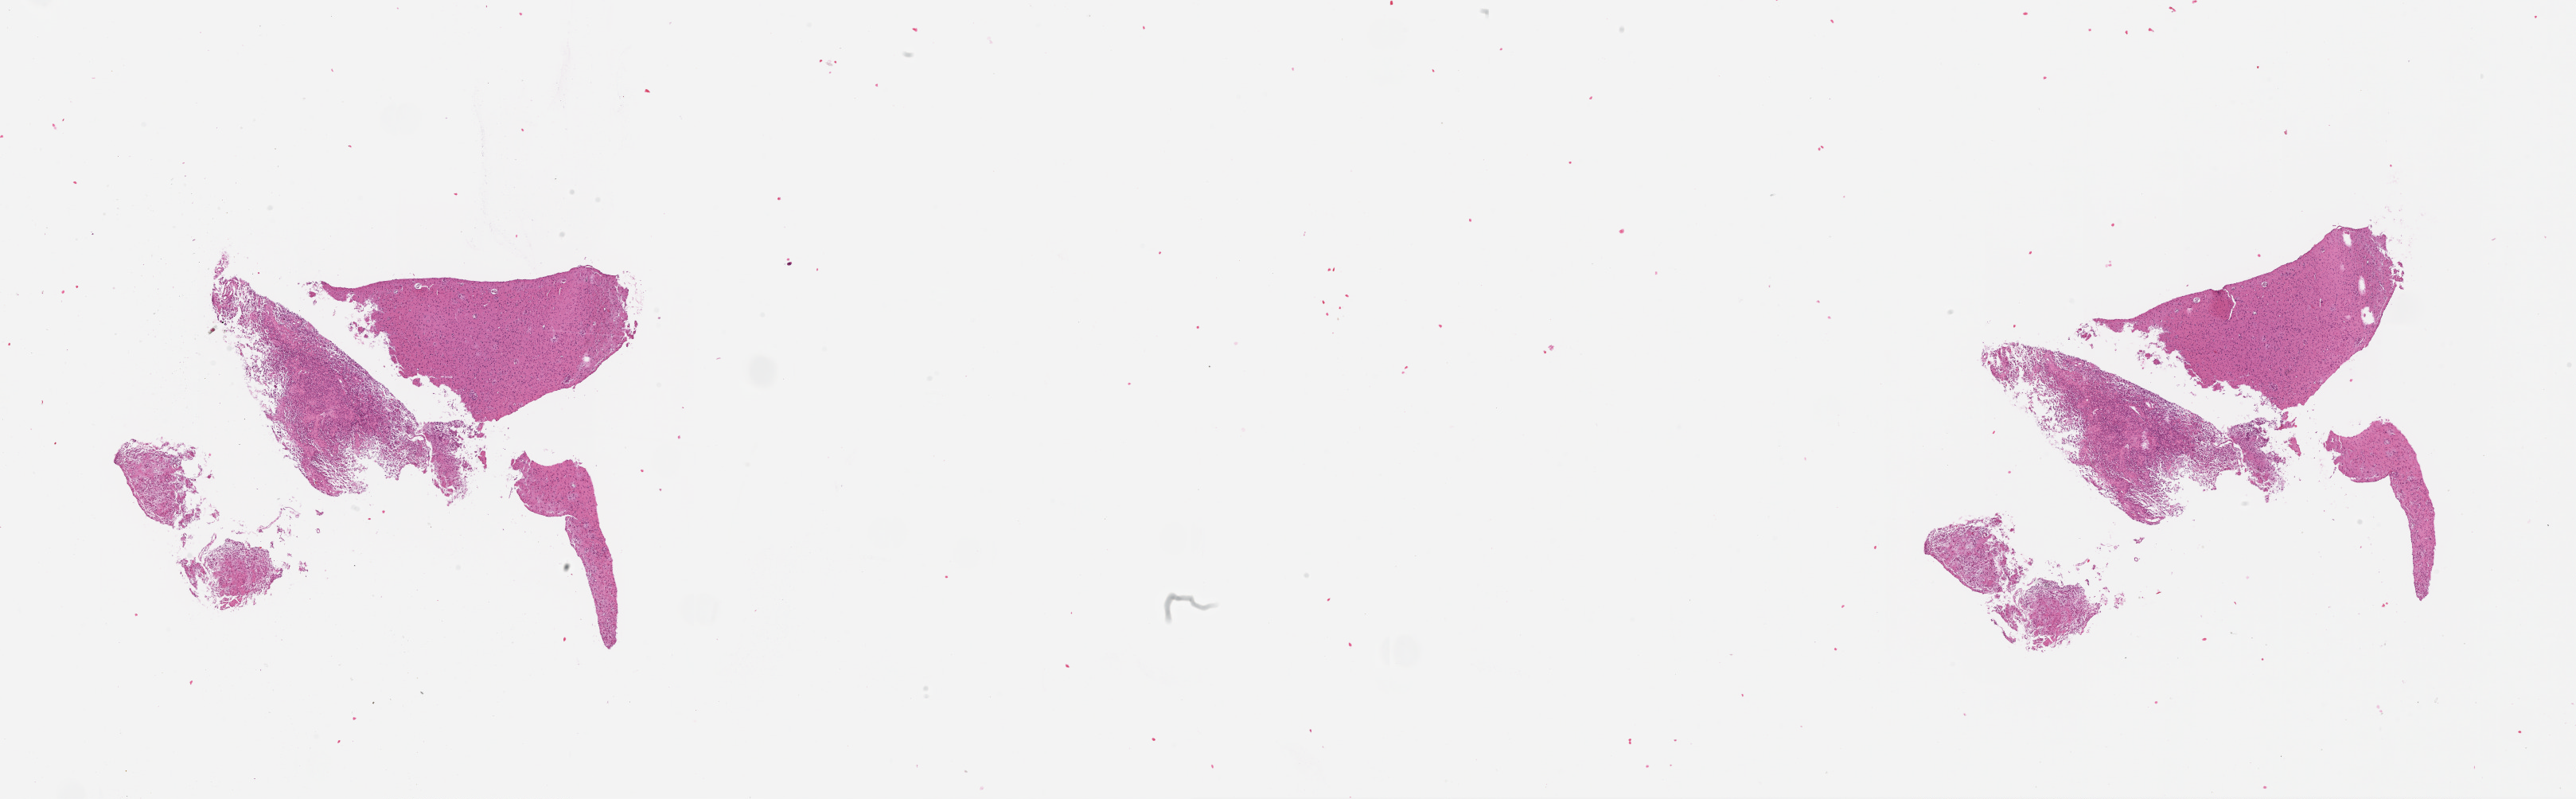
Digitized Hematoxylin and eosin (H&E) stained tissue section (whole slide), shown as a low-resolution overview of the whole scanned area (about 26.1 x 8.1 mm, from a 20x scan), brain, tumour tissue. 66-year-old male patient.
Primary tumour site (as recorded): temporal lobe. Diagnosis: Glioblastoma.